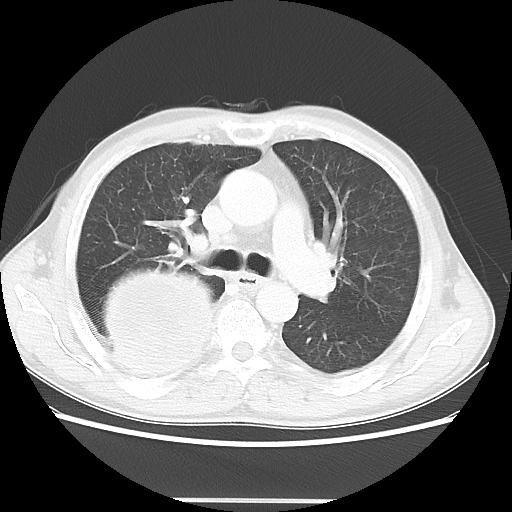
Chest CT, one axial slice; slice 31 of 48 in the series (ordered by position); reconstruction kernel LUNG; 100 kVp; lung window (W 1500 / L -600 HU); 5 mm slice thickness; 512 × 512 image matrix. Patient: male, 66 years. Case-level facts recorded for this patient, not image findings: clinical TNM (as recorded): T4 N1 M1; histopathological grade: G3.
Outlined on this slice (bounding box drawn by a radiologist):
- lung tumour (recorded histology: small cell carcinoma): bounding box (x1, y1, x2, y2) in pixels: (91, 259, 224, 386)